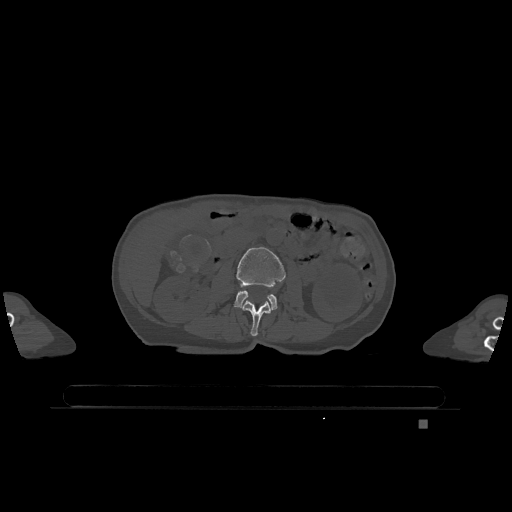
CT including the spine, one axial slice; position 384 of 1317 along the scan axis; bone window (W 1800 / L 400 HU); 512 × 512 image matrix, field of view 500 × 500 mm. Female patient, age 74 years. Case-level facts recorded for this patient, not image findings: primary cancer: lung; vertebrae with lytic lesions (as recorded): T1, T4, T5, T6, L4, L5.
Structures marked on this image (semi-automatic segmentation, software-assisted and operator-edited):
- L2 vertebra: bounding box (x1, y1, x2, y2) in pixels: (242, 300, 271, 336)
- L3 vertebra: (234, 247, 286, 311)